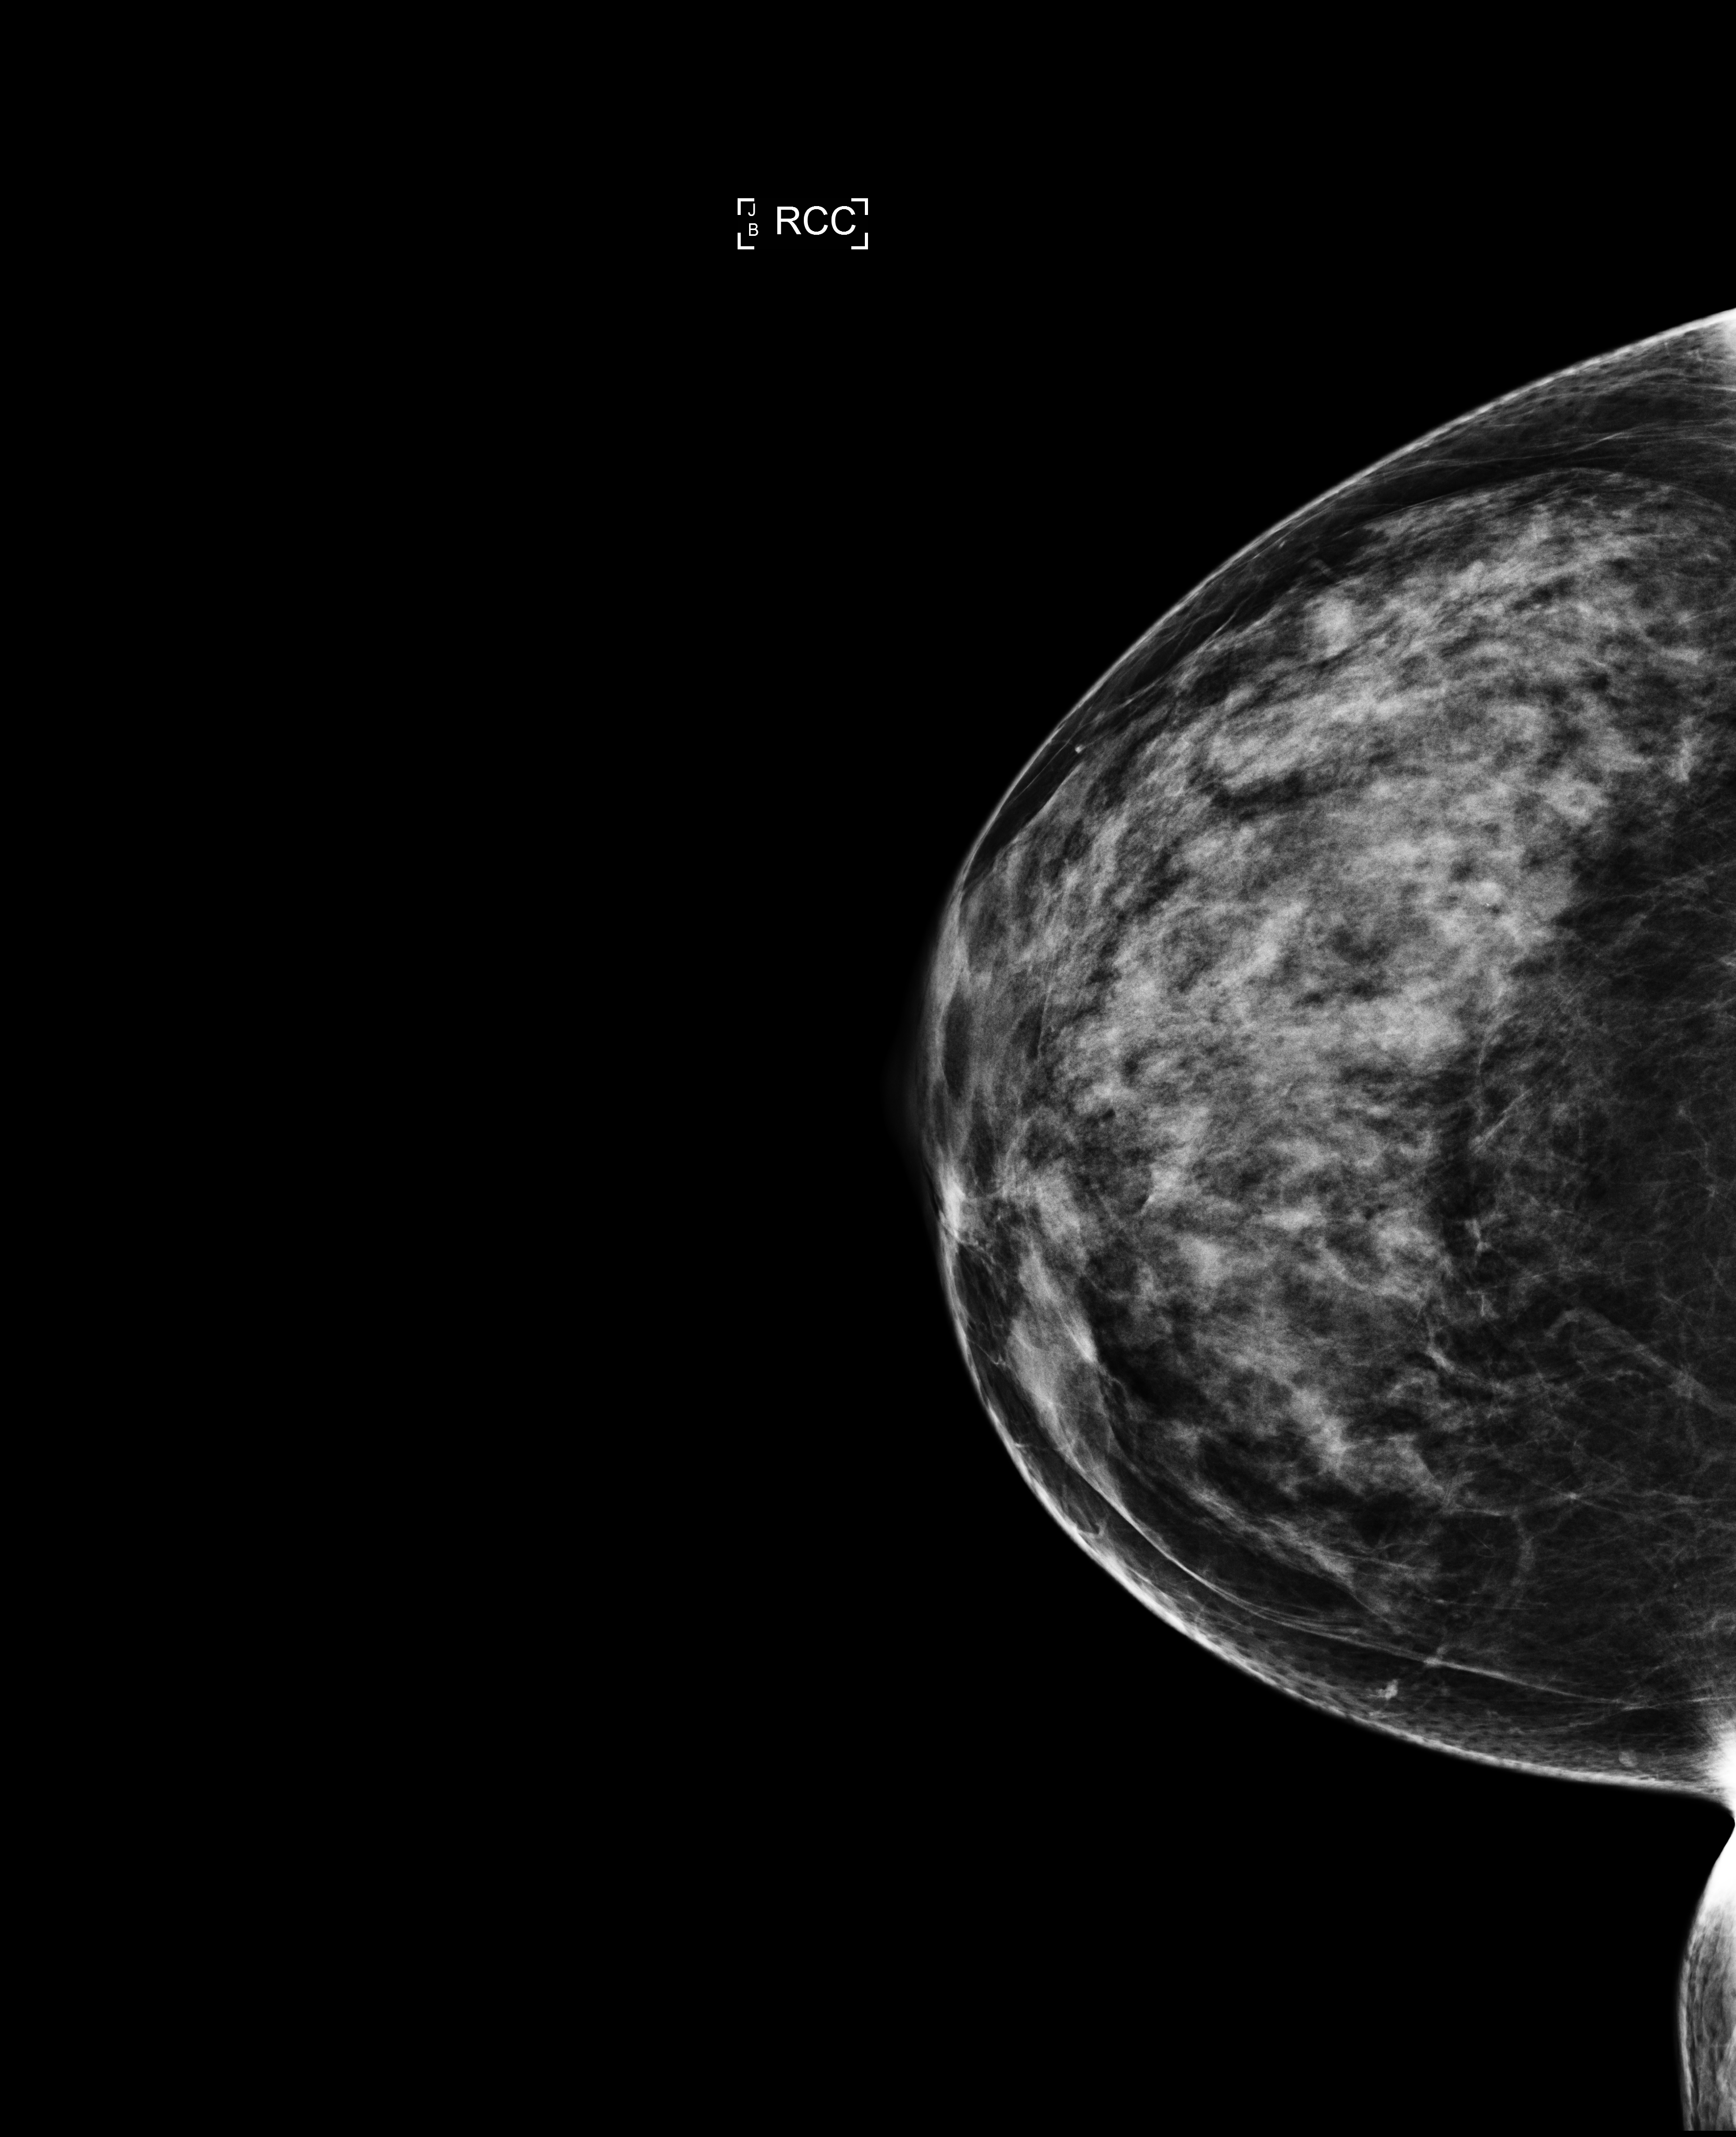
Annual screening mammography examination. Patient aged 42 years (female).
Image type: full-field digital mammogram. Breast: right. Projection: craniocaudal (CC) view.